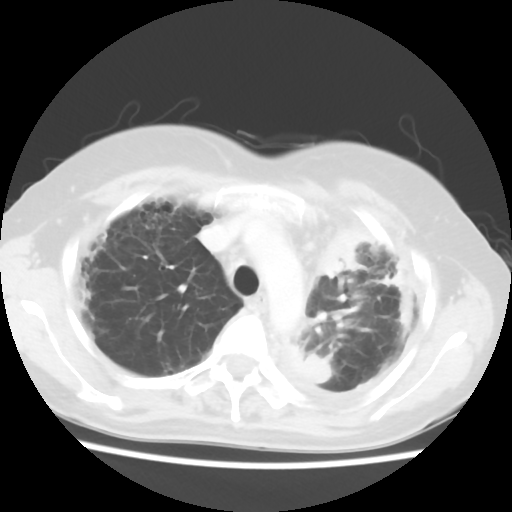
Chest CT, one axial slice; slice 42 of 56 in the series (ordered by position); lung window (W 1500 / L -600 HU); 5 mm slice thickness; 512 × 512 image matrix. Patient: female, 56 years. Case-level facts recorded for this patient, not image findings: clinical TNM (as recorded): T1c N0 M1.
Annotated regions visible in this slice (rectangle marked by the reading radiologist):
- lung tumour (recorded histology: adenocarcinoma): bounding box <322,229,365,283> (left, top, right, bottom; pixels)